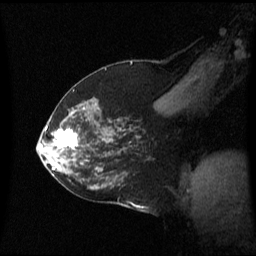
Breast MRI (dynamic contrast-enhanced), one sagittal slice; position 38 of 60 along the scan axis; dynamic contrast-enhanced series, image 2 of 3 at this slice position (ordered by acquisition); 1.5 T; TE 4.2 ms, TR 8.4 ms; 2 mm slice thickness; 256 × 256 image matrix. Patient: female, 59 years. Case-level facts recorded for this patient, not image findings: setting: breast cancer imaged before/during neoadjuvant chemotherapy; receptor status: HR-positive, HER2-negative.
Annotated regions visible in this slice (semi-automatically segmented with operator editing):
- analysis volume of interest (the breast-tissue region the enhancement analysis was run in; not a lesion): bounding box [x1, y1, x2, y2] px = [46, 114, 89, 163]
- tumour enhancement mask (voxels above the 70 % enhancement threshold inside the analysis volume of interest): [54, 130, 77, 149]